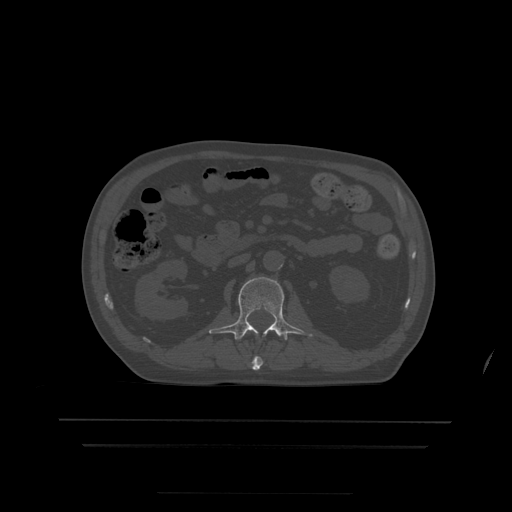
CT including the spine, one axial slice. Position 148 of 522 along the scan axis. Bone window (W 1800 / L 400 HU). 1.25 mm slice thickness. 512 × 512 image matrix. Patient age 68 years. Case-level facts recorded for this patient, not image findings: primary cancer: urothelial.
Annotated regions visible in this slice (semi-automatically segmented with operator editing):
- L1 vertebra: bounding box (x1, y1, x2, y2) in pixels: (252, 356, 263, 371)
- L2 vertebra: (209, 277, 313, 340)